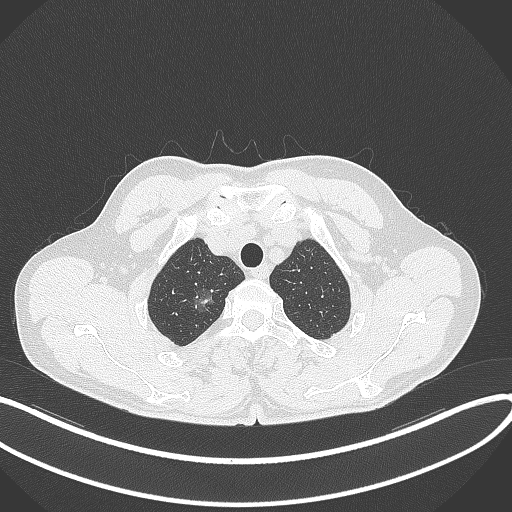
Chest CT, one axial slice; slice 335 of 407 in the series (ordered by position); reconstruction kernel B70f; 120 kVp; lung window (W 1500 / L -600 HU); 1 mm slice thickness; 512 × 512 image matrix, field of view 400 × 400 mm. Male patient, age 58 years. From the clinical record (not read from this slice): clinical TNM (as recorded): T1c N0 M0; histopathological grade: G1-2.
Structures marked on this image (rectangle marked by the reading radiologist):
- lung tumour (recorded histology: adenocarcinoma): bounding box [x1, y1, x2, y2] px = [184, 281, 223, 321]